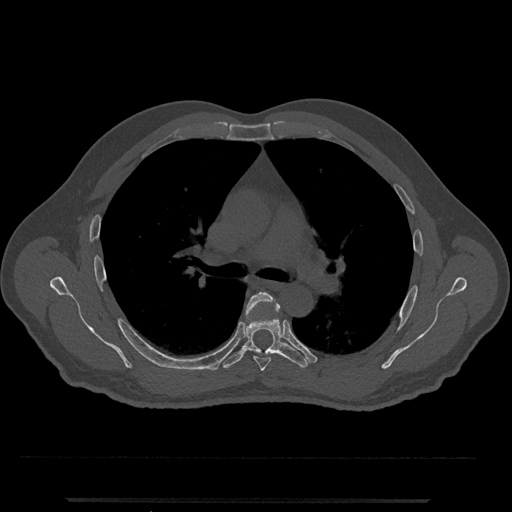
CT including the spine, one axial slice. Position 762 of 797 along the scan axis. Reconstruction kernel Br40s/3. Bone window (W 1800 / L 400 HU). 0.5 mm slice thickness. 512 × 512 image matrix. Patient: male, 63 years. Case-level facts recorded for this patient, not image findings: primary cancer: prostate.
Outlined on this slice (semi-automatic segmentation, software-assisted and operator-edited):
- T5 vertebra: bounding box <245,292,280,371> (left, top, right, bottom; pixels)
- T6 vertebra: <221,298,310,369>